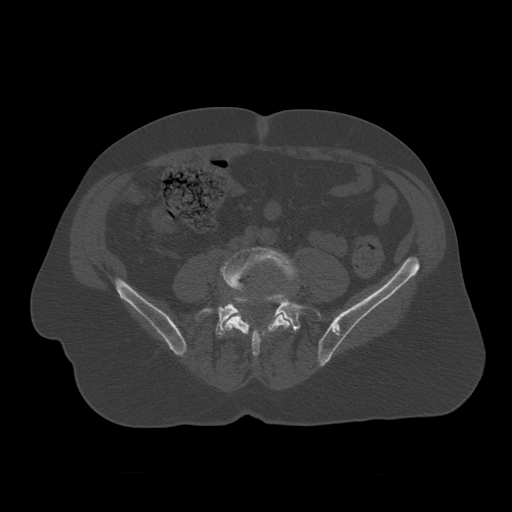
CT including the spine, one axial slice. Slice 265 of 450 in the series (ordered by position). Reconstruction kernel STANDARD. Bone window (W 1800 / L 400 HU). 1.25 mm slice thickness. 512 × 512 image matrix, field of view 405 × 405 mm. Patient age 75 years. Case-level facts recorded for this patient, not image findings: primary cancer: prostate.
Structures marked on this image (semi-automatic segmentation, software-assisted and operator-edited):
- L4 vertebra: bounding box [x1, y1, x2, y2] px = [221, 247, 298, 357]
- L5 vertebra: [196, 293, 322, 339]